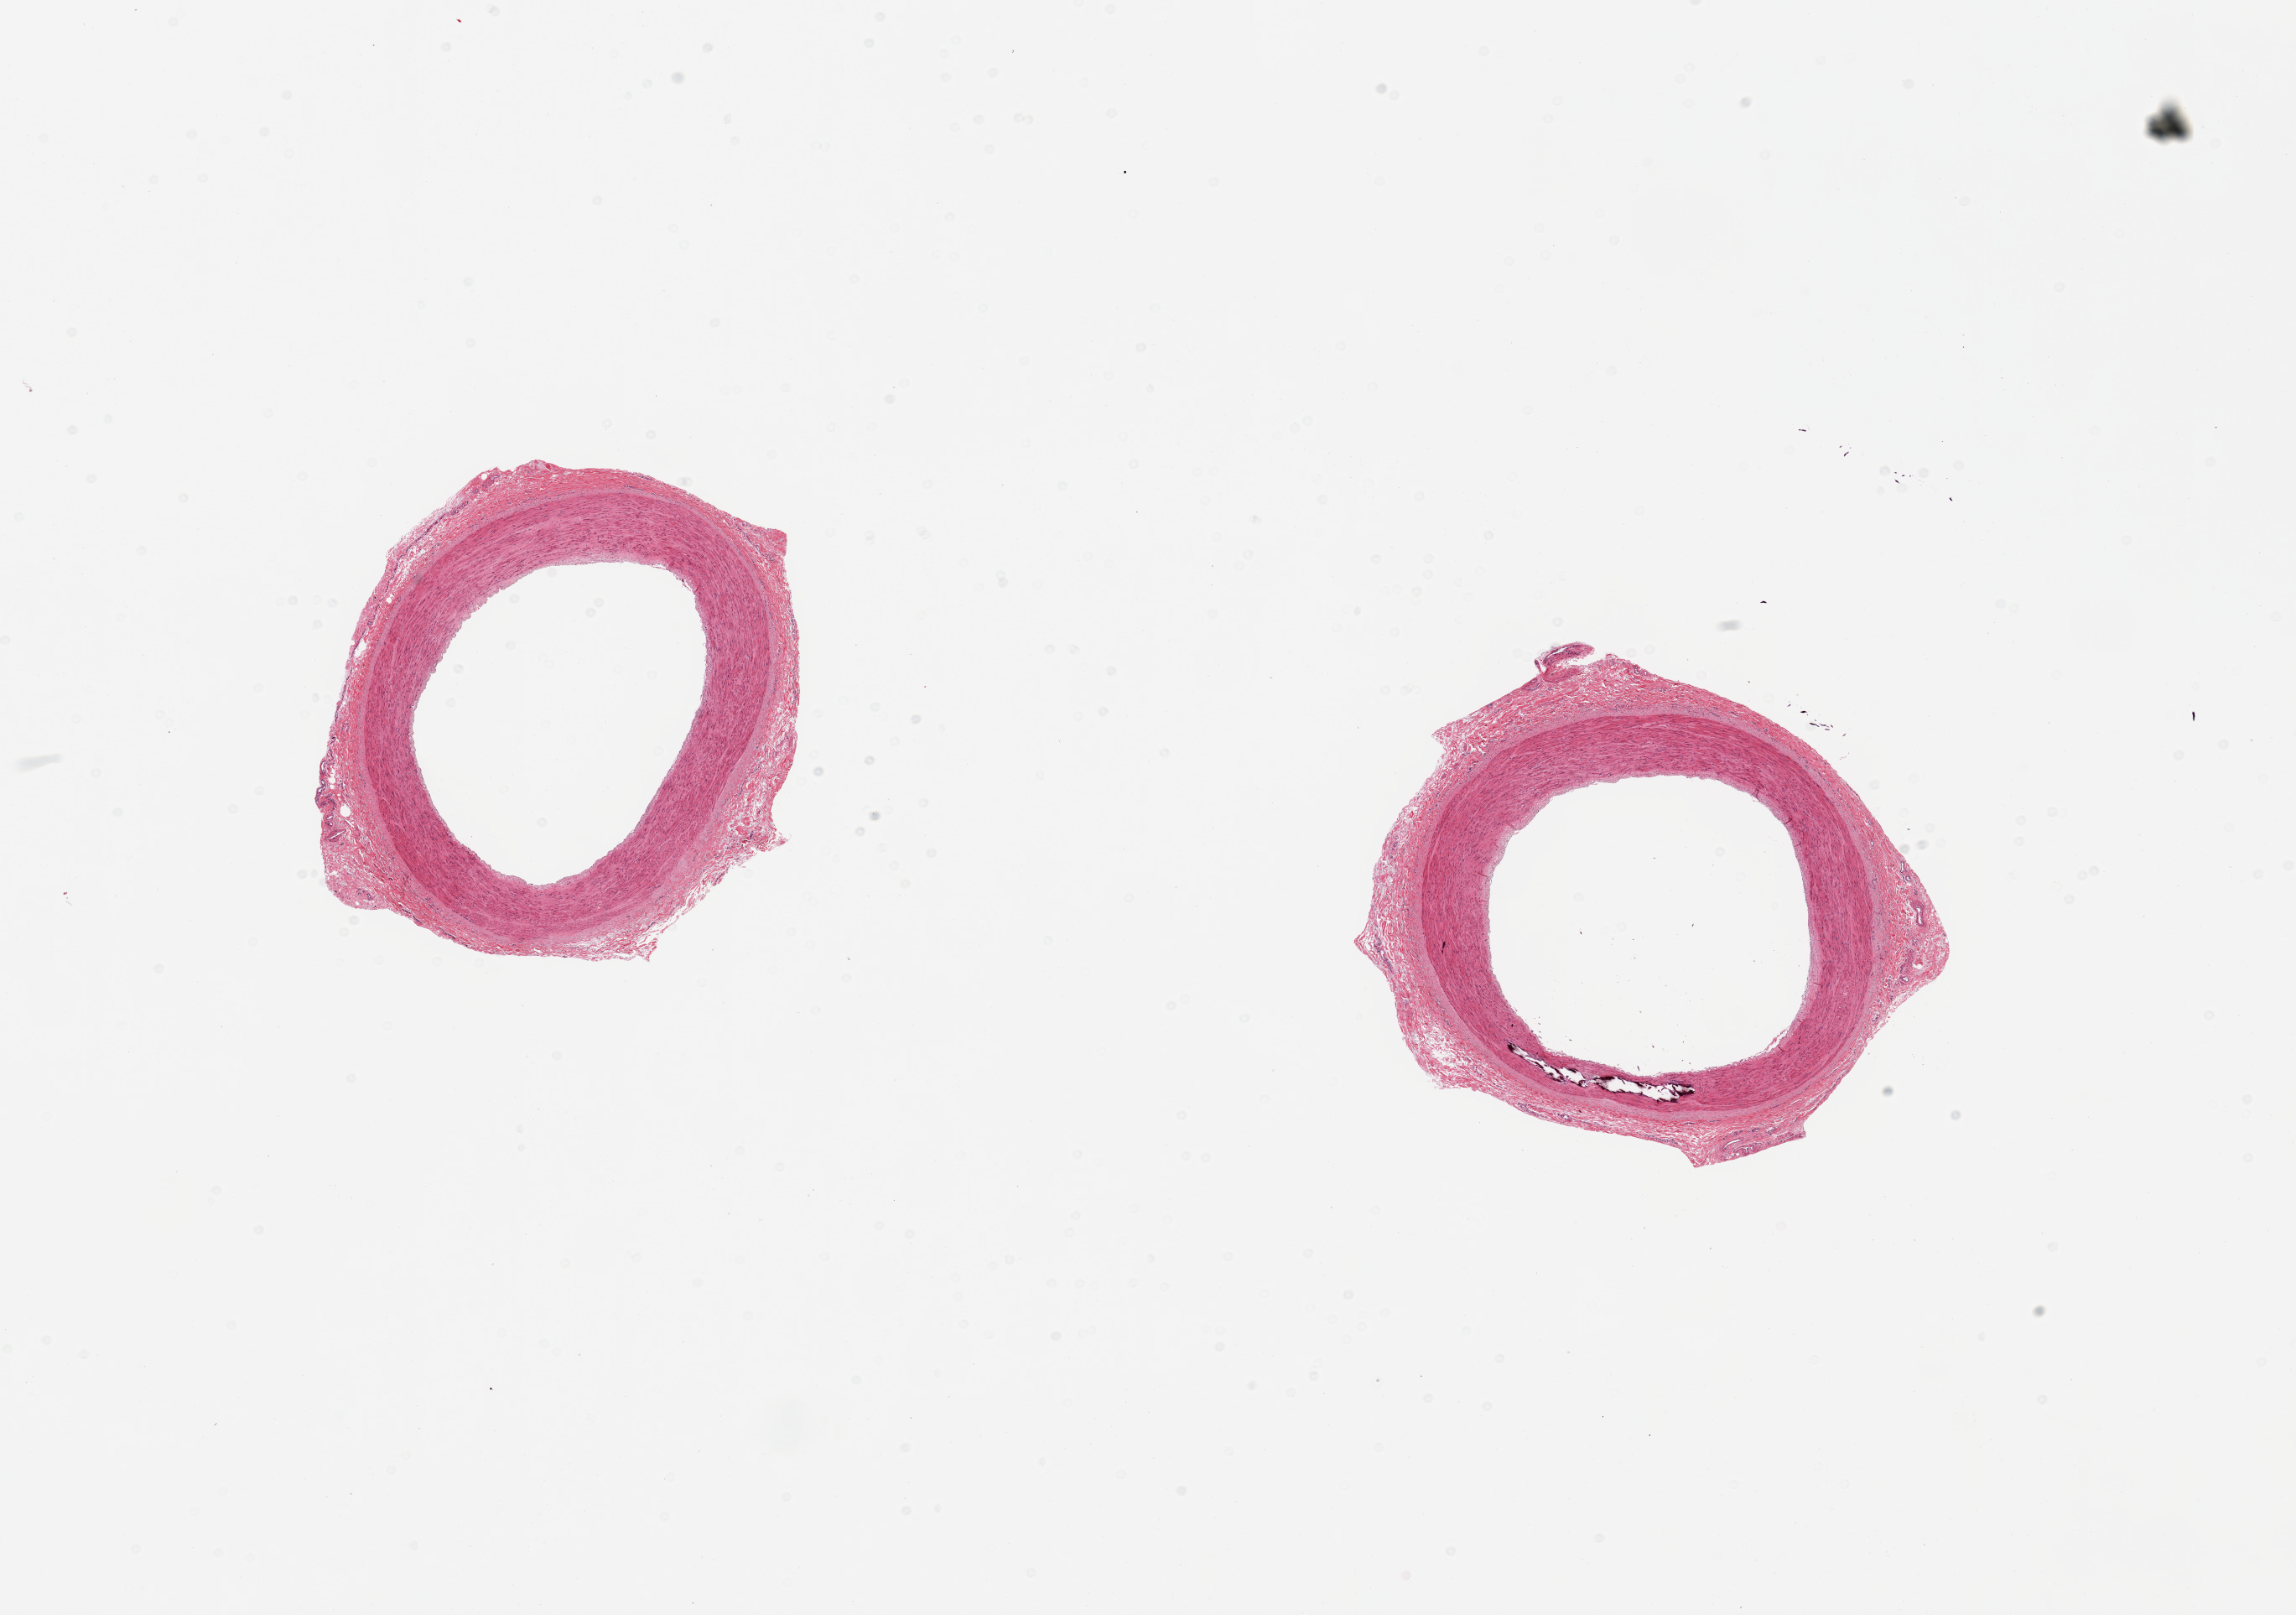
Digitized hematoxylin and eosin (H&E)-stained section, shown as a low-resolution overview of the whole scanned area (about 21.7 x 15.2 mm, acquisition: 20x scan); PAXgene-fixed, paraffin-embedded tissue; section of tibial artery (target tissue); tissue donor sample. Donor sex: male.
• reviewer comment on this tissue sample: 2 pieces, no atherosis; focal Monckeberg medial sclerosis, clean sections